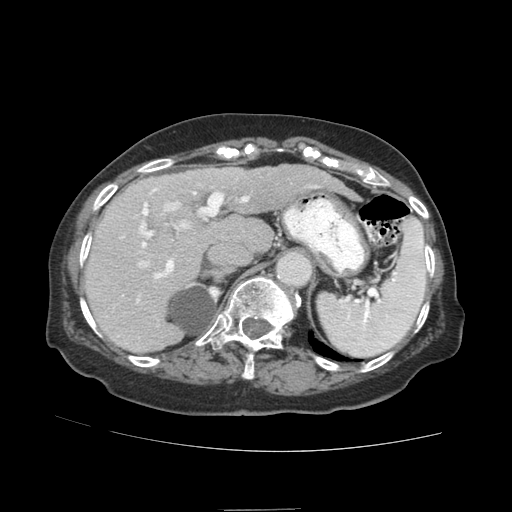
Contrast-enhanced abdominal CT (liver protocol), one axial slice. Slice 61 of 89 in the series (ordered by position). 140 kVp. Soft-tissue window (W 400 / L 40 HU). 2.5 mm slice thickness. 512 × 512 image matrix. Case-level facts recorded for this patient, not image findings: diagnosis: hepatocellular carcinoma (patient treated with transarterial chemoembolisation; whether this scan precedes or follows treatment is not stated here); TNM stage (as recorded): Stage-II; Child-Pugh class: A; tumour differentiation: moderately differentiated; tumour nodularity: multinodular.
Structures marked on this image (semi-automatic segmentation, software-assisted and operator-edited):
- liver parenchyma outside the tumour (the mass and vessels are separate outlines, so this box may not span the whole liver): box from (x=84, y=164) to (x=322, y=352) px
- mass: (x=255, y=168)–(x=274, y=183)
- liver vessels: (x=118, y=178)–(x=318, y=337)